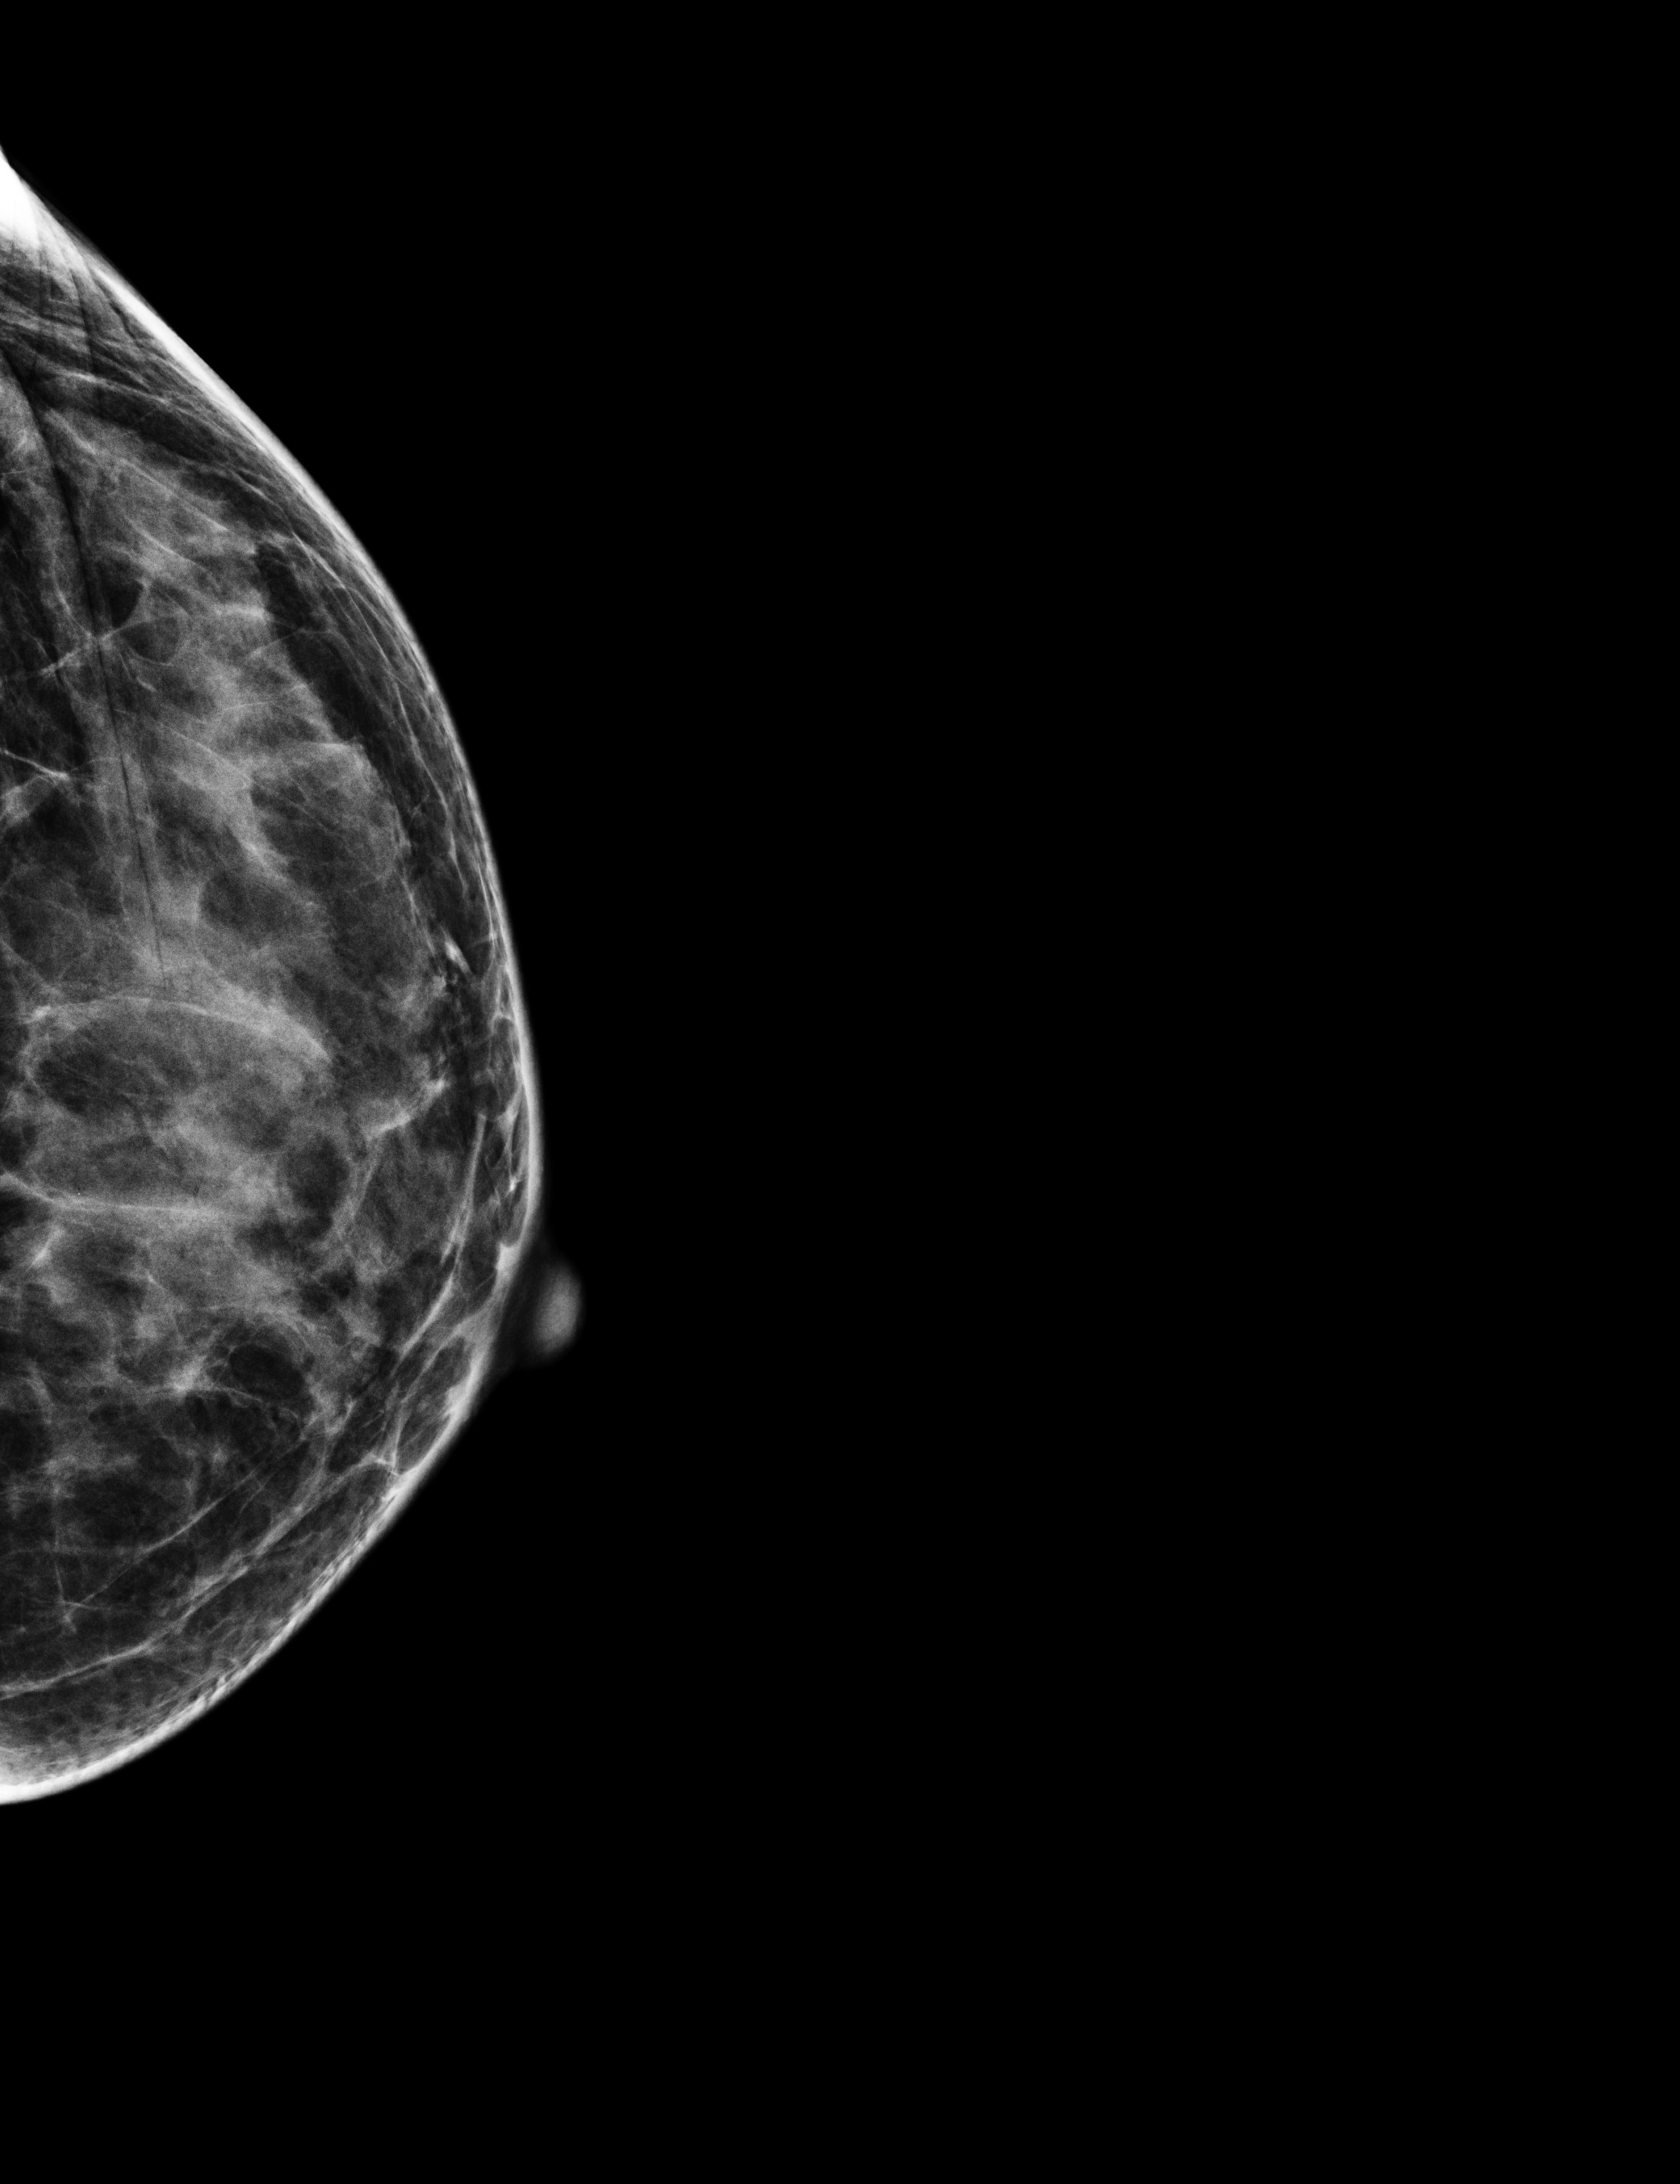
Digital mammogram (FFDM); left breast; exaggerated CC view (lateral); annual screening mammography examination; compressed breast thickness 32 mm; system: Selenia Dimensions. Female patient, age 52 years.
Final BI-RADS category for the screening round (tomosynthesis exam, both breasts): category 1.